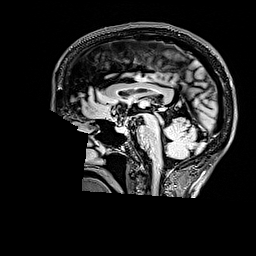
Brain MRI from a brain-tumour surgery series, one sagittal slice; position 91 of 176 along the scan axis; T2 FLAIR; 1 mm slice thickness; 256 × 256 image matrix, field of view 256 × 256 mm. Case-level facts recorded for this patient, not image findings: histopathology: Astrocytoma; WHO grade: 3; IDH mutation: yes; tumour location: Right Parietal.
Structures marked on this image (expert manual segmentation):
- tumour: bounding box (x1, y1, x2, y2) in pixels: (190, 60, 201, 69)
- tumour: (191, 63, 193, 66)